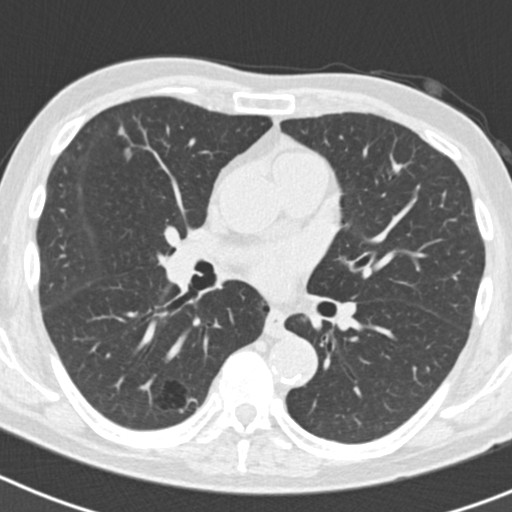
Axial slice from a low-dose chest CT screening exam; second annual screen; lung window (W 1500 / L -600 HU); 2 mm slice thickness. Male participant, aged 70 years at enrolment. Current smoker at enrolment.
- Expert-annotated lung lesion, bounding box <130,369,201,432> (left, top, right, bottom; pixels).
- The screening reader recorded 5 non-calcified nodules or masses ≥4 mm on this exam; which of them this box marks is not recorded.
- Later outcome: lung cancer diagnosed 622 days after this screen (after the third annual screen) — bronchiolo-alveolar adenocarcinoma, NOS, right lower lobe, poorly differentiated (G3), stage IB (AJCC 6th edition), 30 mm at pathology.